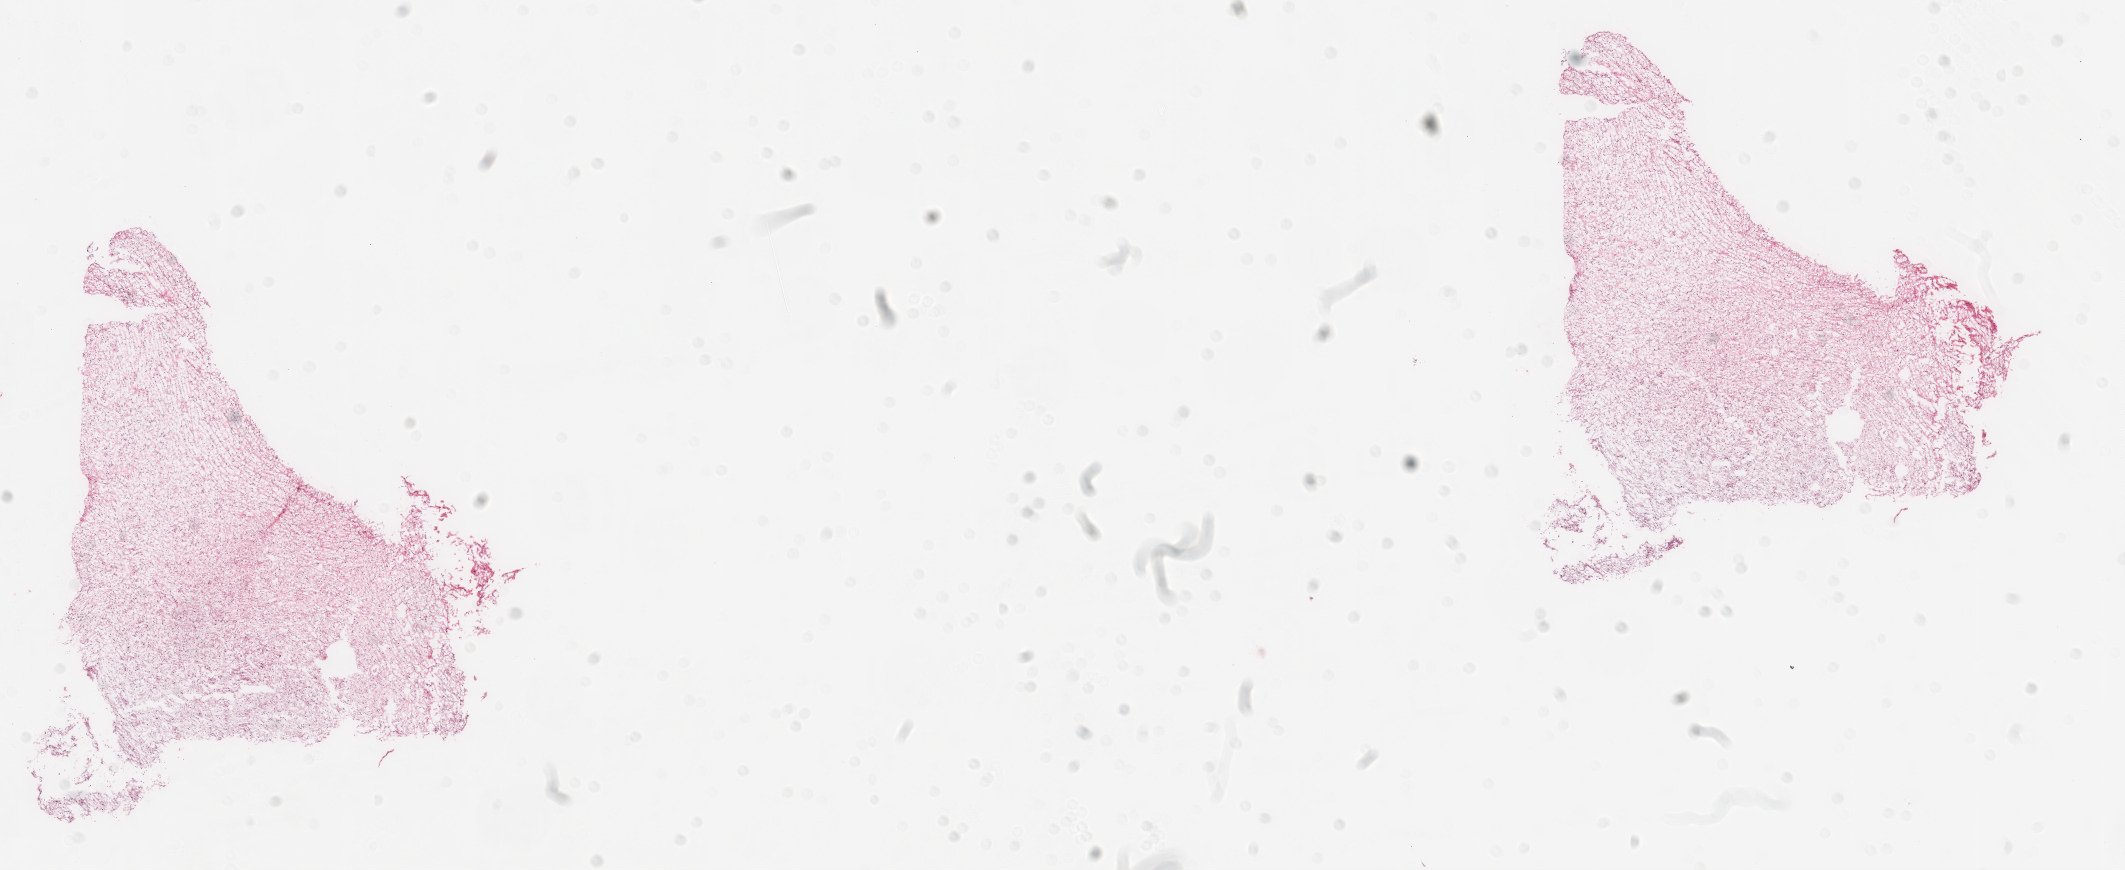
H&E-stained whole-slide image, a low-resolution overview of the entire scanned area, about 17.1 x 7.0 mm (acquisition: 20x scan). Frozen section from the top of the tissue portion. Sample: primary tumour, brain. Patient: male, age at initial diagnosis 39 years. Composition of this section per pathologist review: tumour cells 100%, tumour nuclei 80%, normal cells 0%, stromal cells 0%, necrosis 0%.
• histologic diagnosis: Glioblastoma